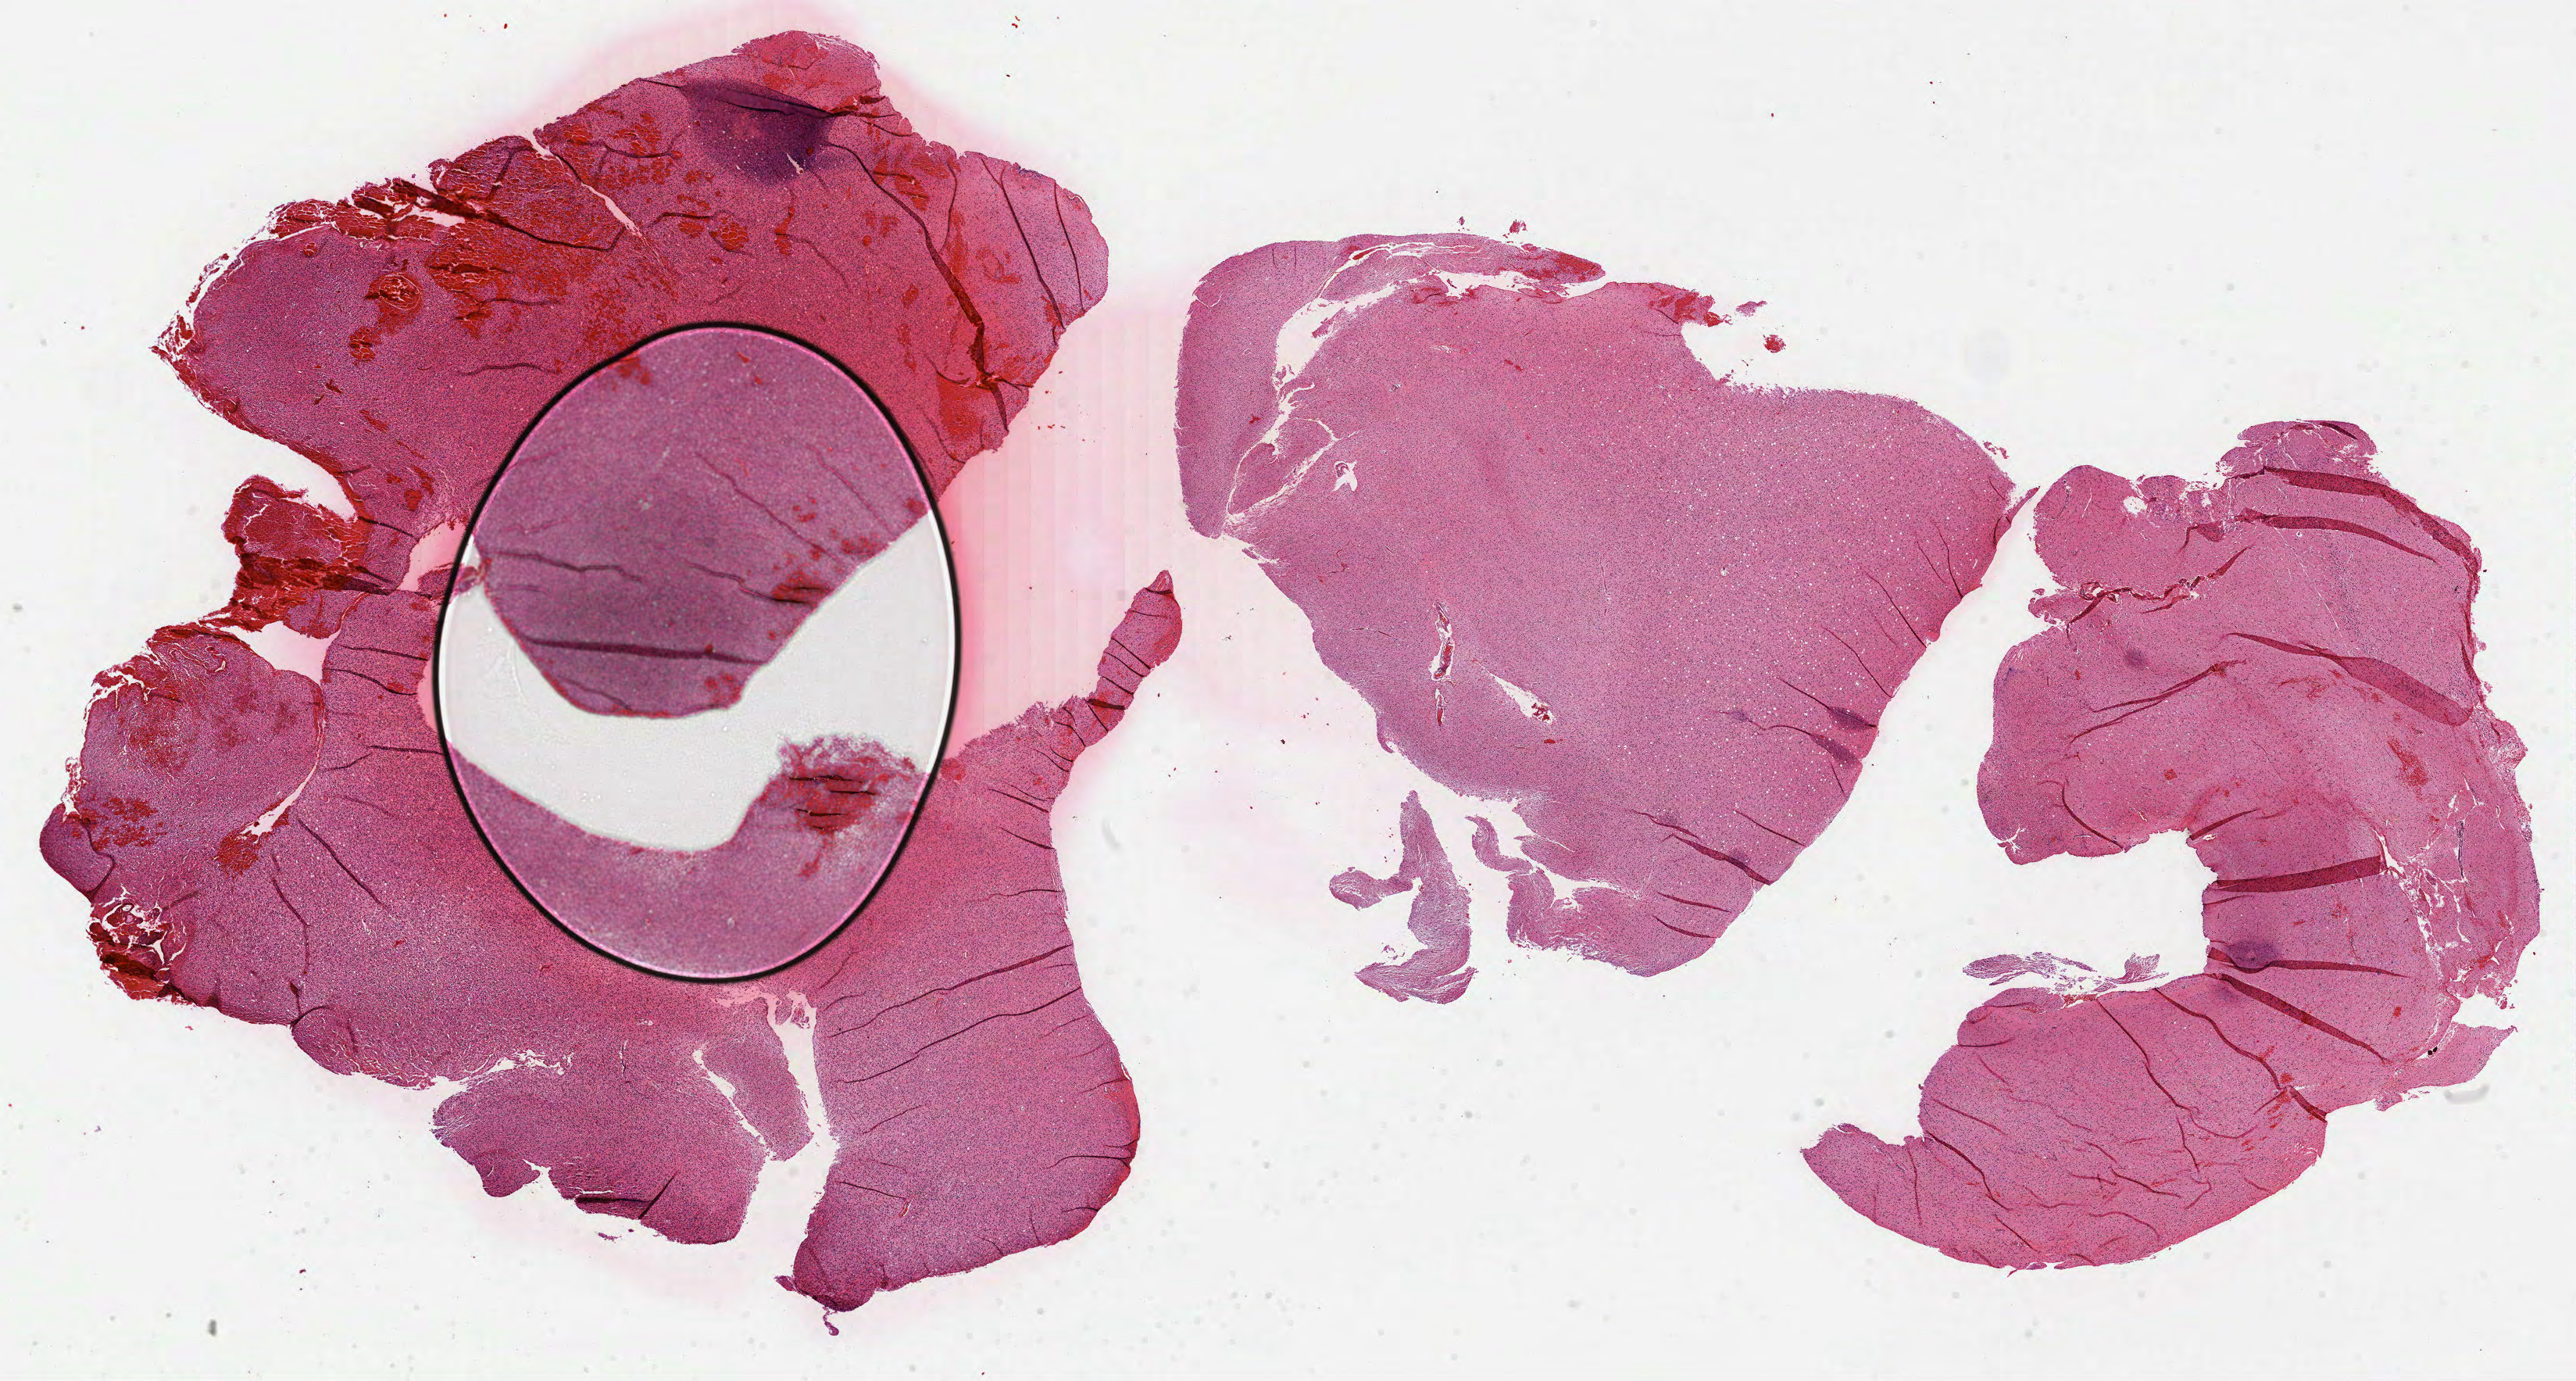
H&E whole-slide image — a low-resolution overview of the entire scanned area, about 26.6 x 14.3 mm (slide scanned at 40x). FFPE section. Primary tumour sample from the brain. Male patient; age at initial diagnosis 50 years. Histologic grade: G2 (moderately differentiated).
Laterality: right. Histologic diagnosis: Astrocytoma, NOS.